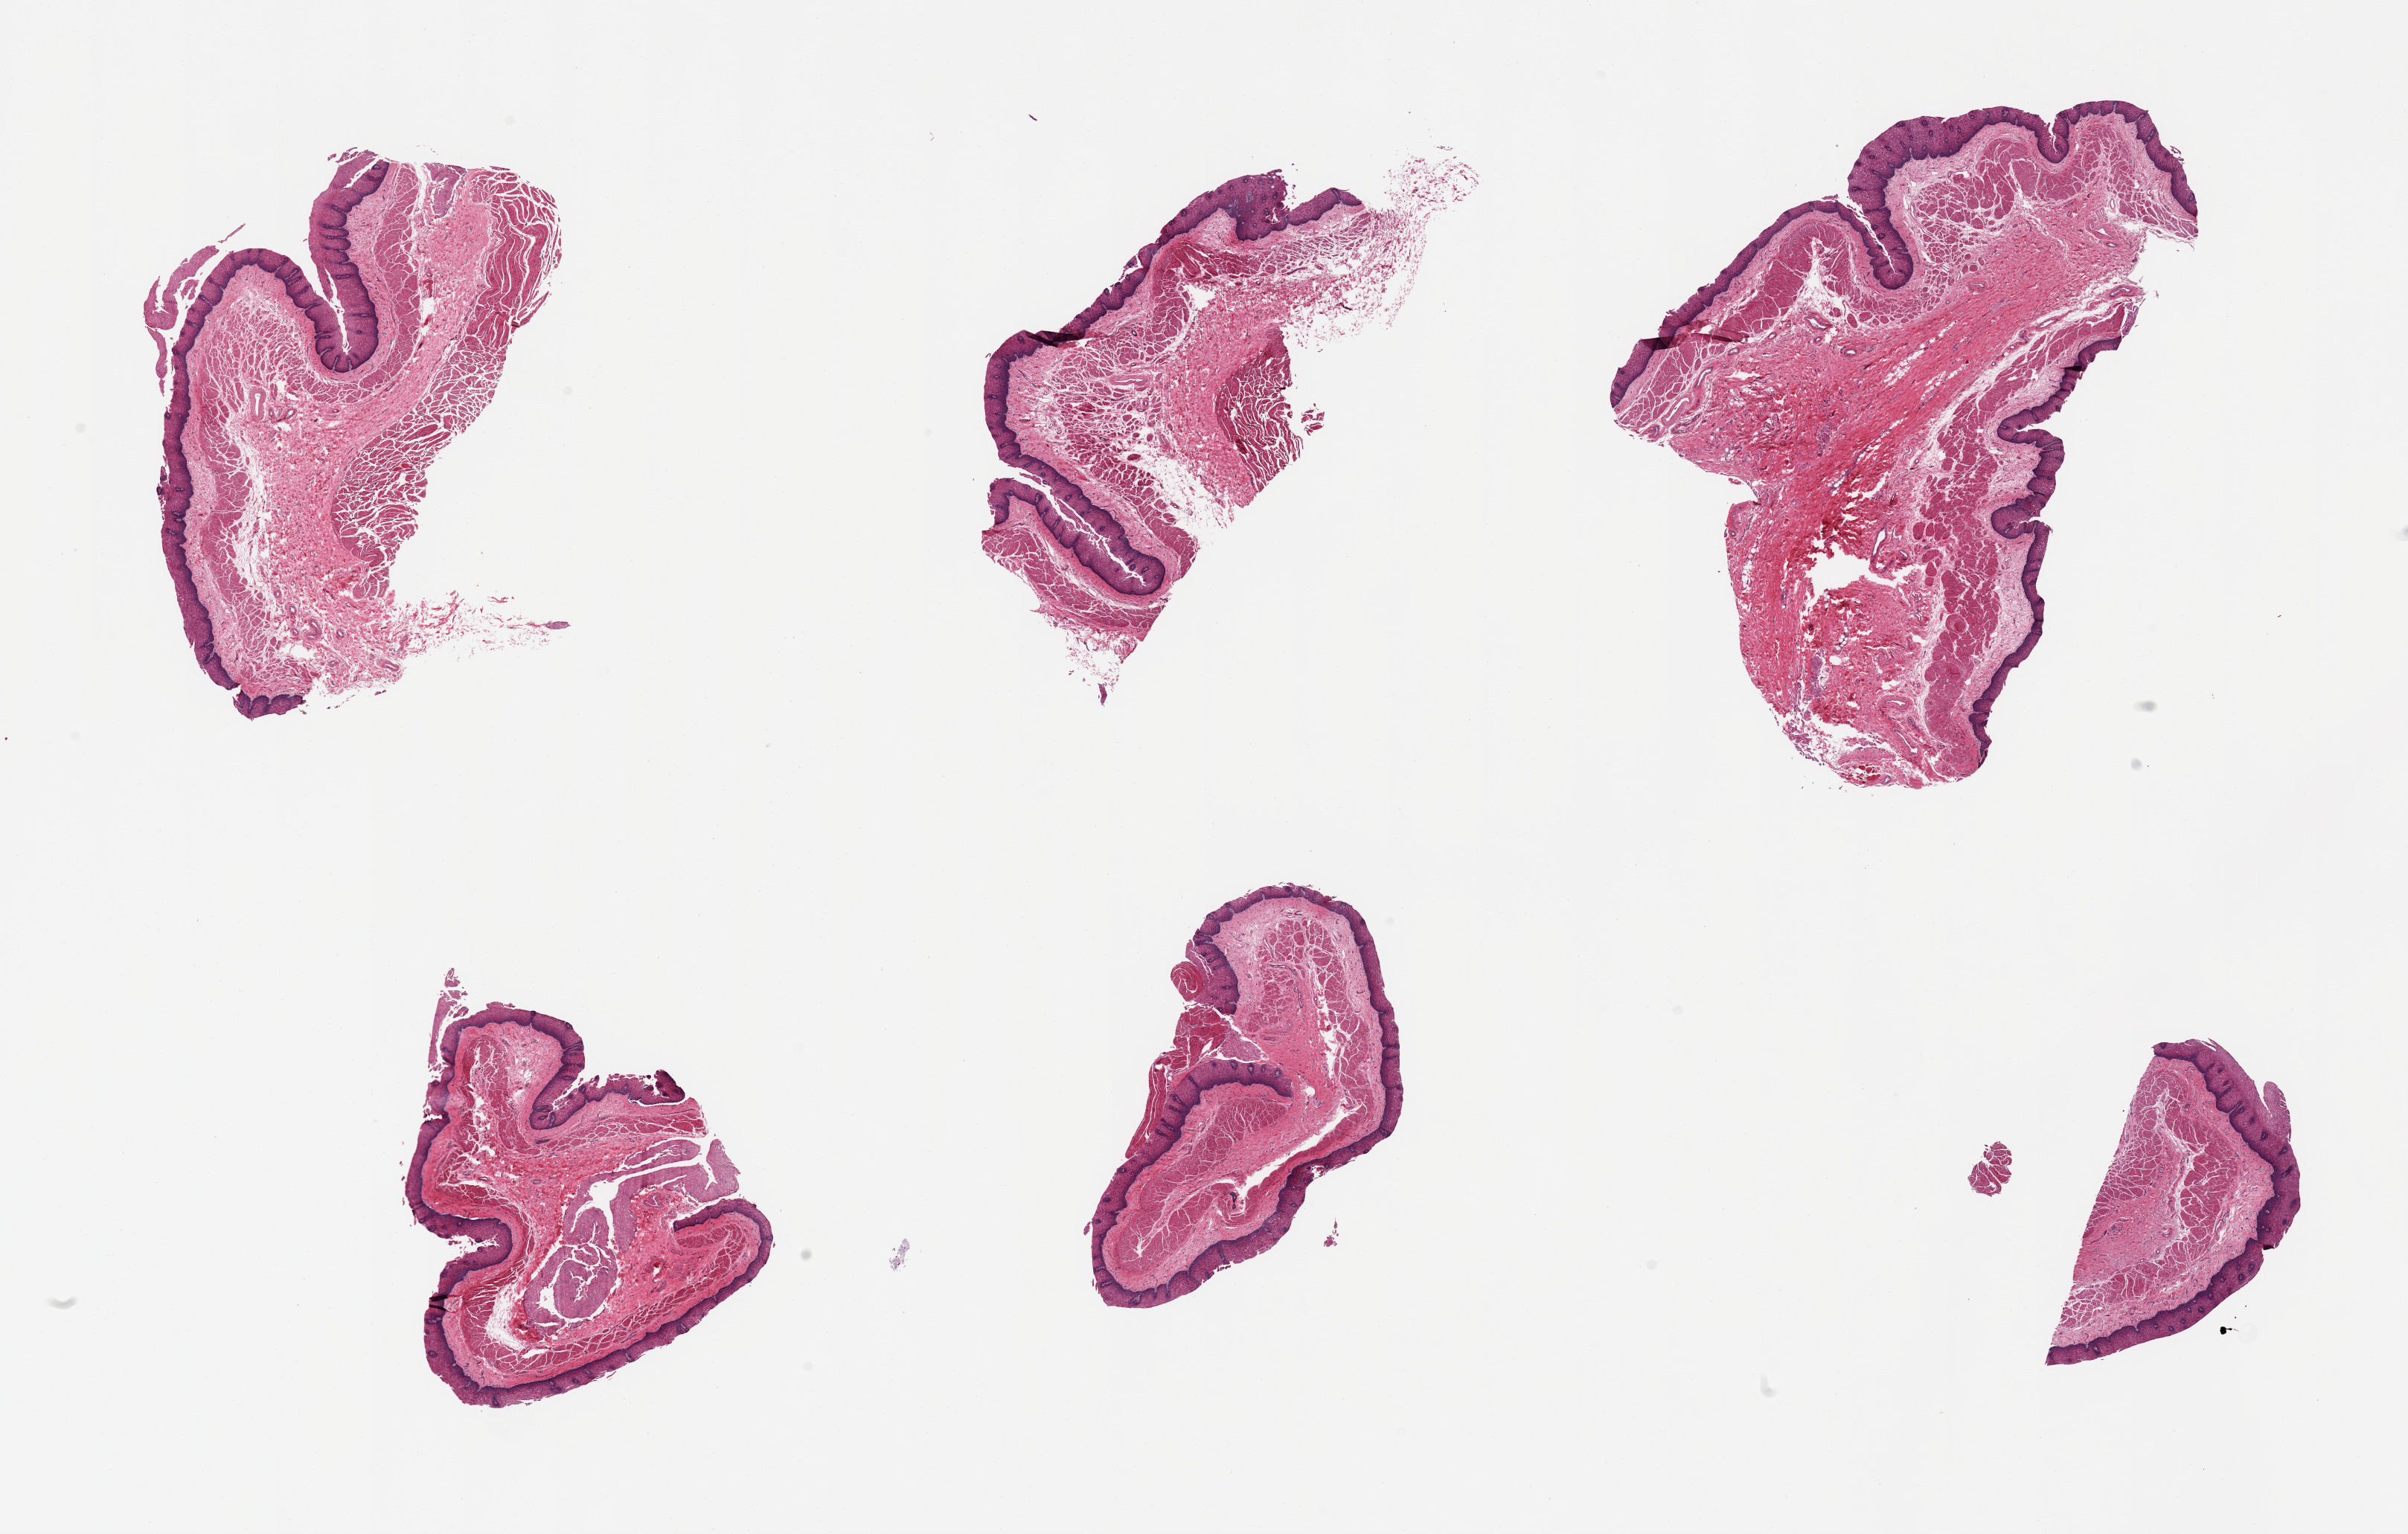
Digitized haematoxylin and eosin-stained section, brightfield — whole scanned area (about 25.6 x 16.3 mm, slide scanned at 20x) shown as a low-resolution overview, PAXgene-fixed paraffin-embedded (PFPE) section, section of esophageal mucous membrane (target tissue), donor tissue sample. Donor sex: female.
- reviewer comment on this tissue sample: 6 pieces; includes small portion of muscularis propria